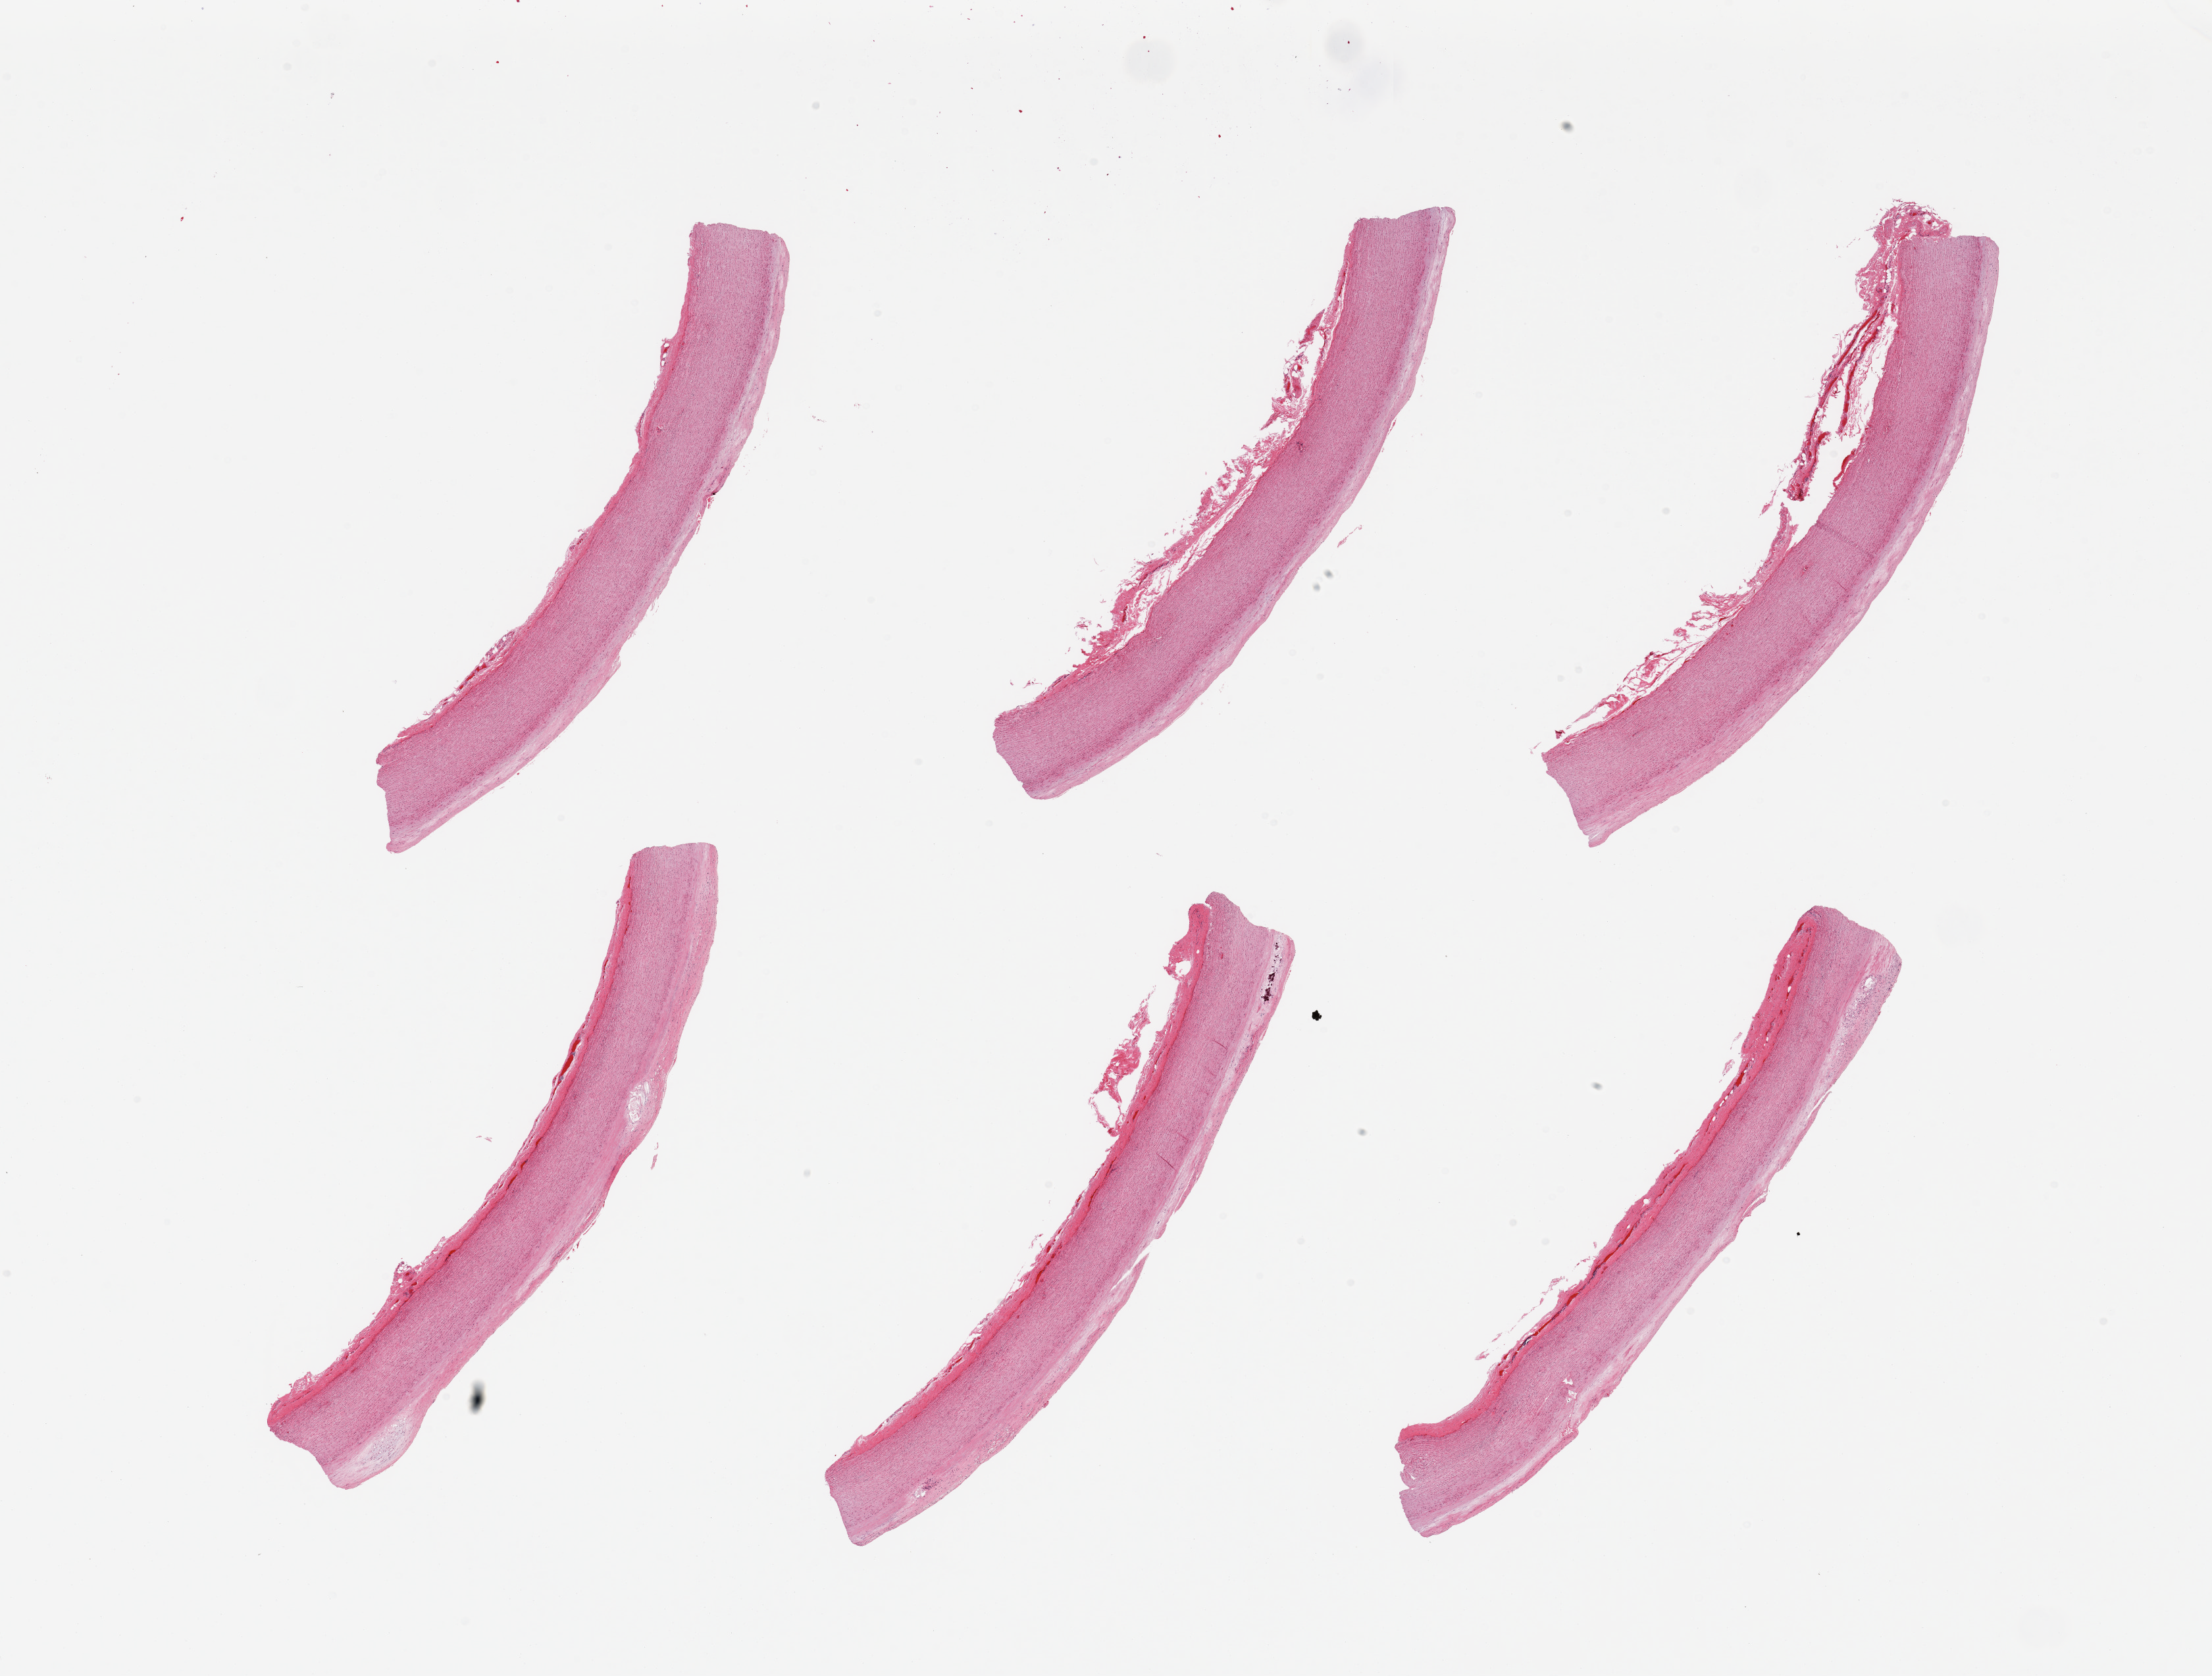
Hematoxylin and eosin (H&E) whole-slide image, whole scanned area (about 26.6 x 20.1 mm) shown as a low-resolution overview; PAXgene-fixed, paraffin-embedded tissue; target tissue: aorta; donor tissue sample. Donor: female.
* pathologist's review note for this sample: 6 pieces, atherosis up to ~0.3mm